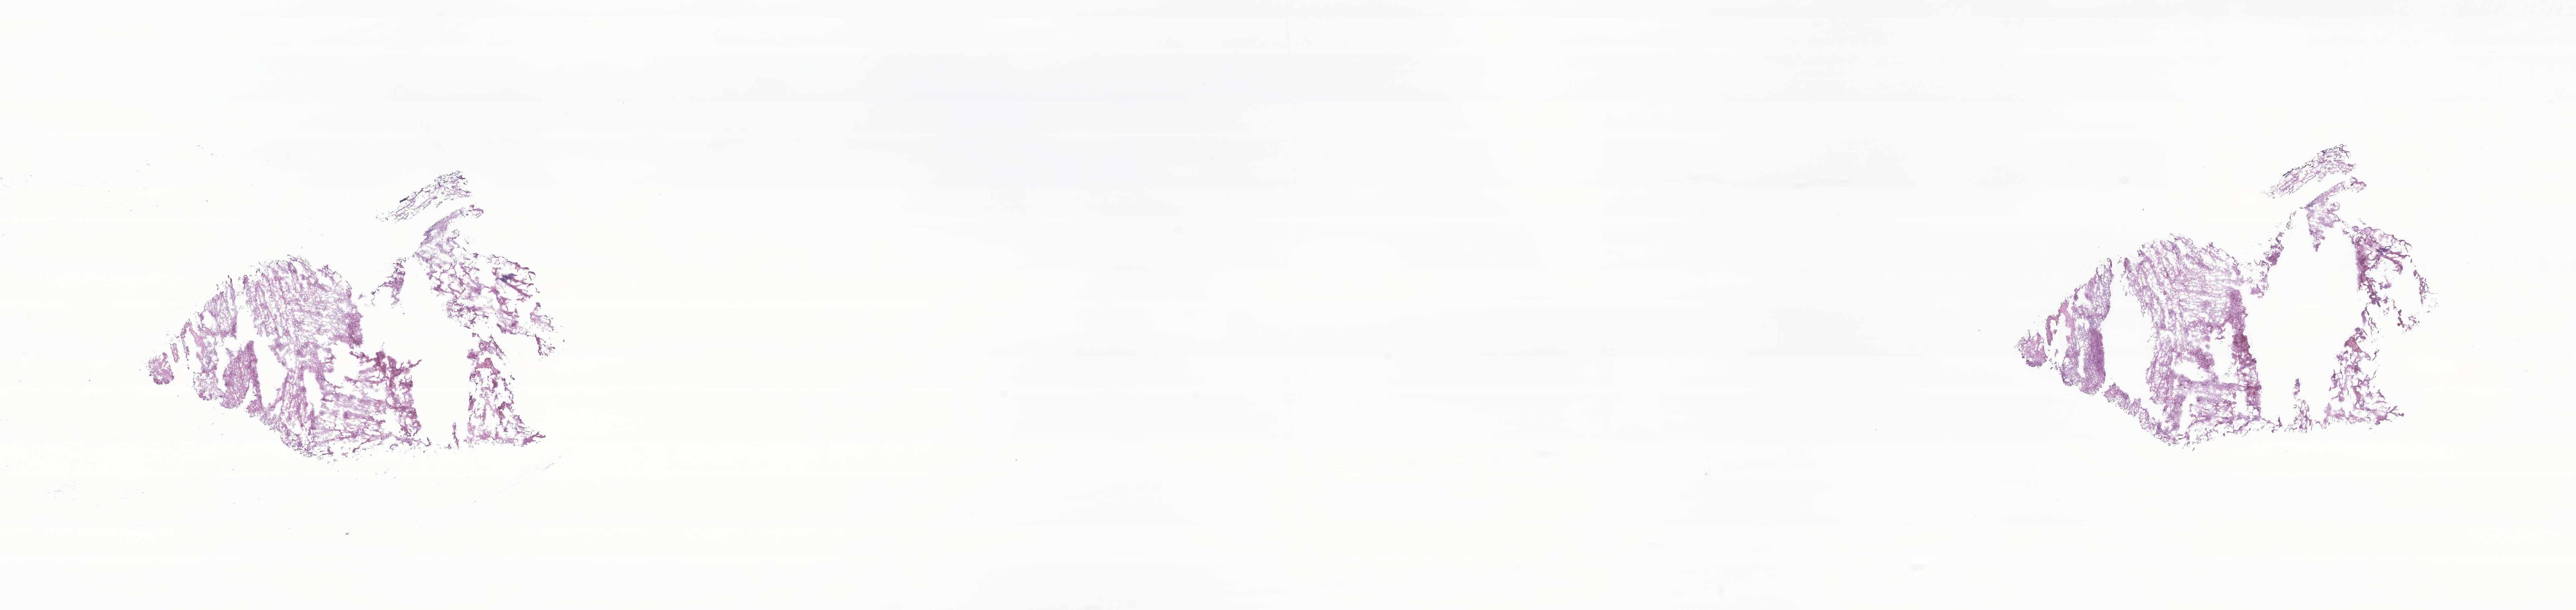
H&E whole-slide image of tumor tissue from the brain — a low-resolution overview of the entire scanned area, about 32.4 x 7.7 mm, frozen section. Female patient, age 43 months.
• diagnosis: Neoplasm, uncertain whether benign or malignant